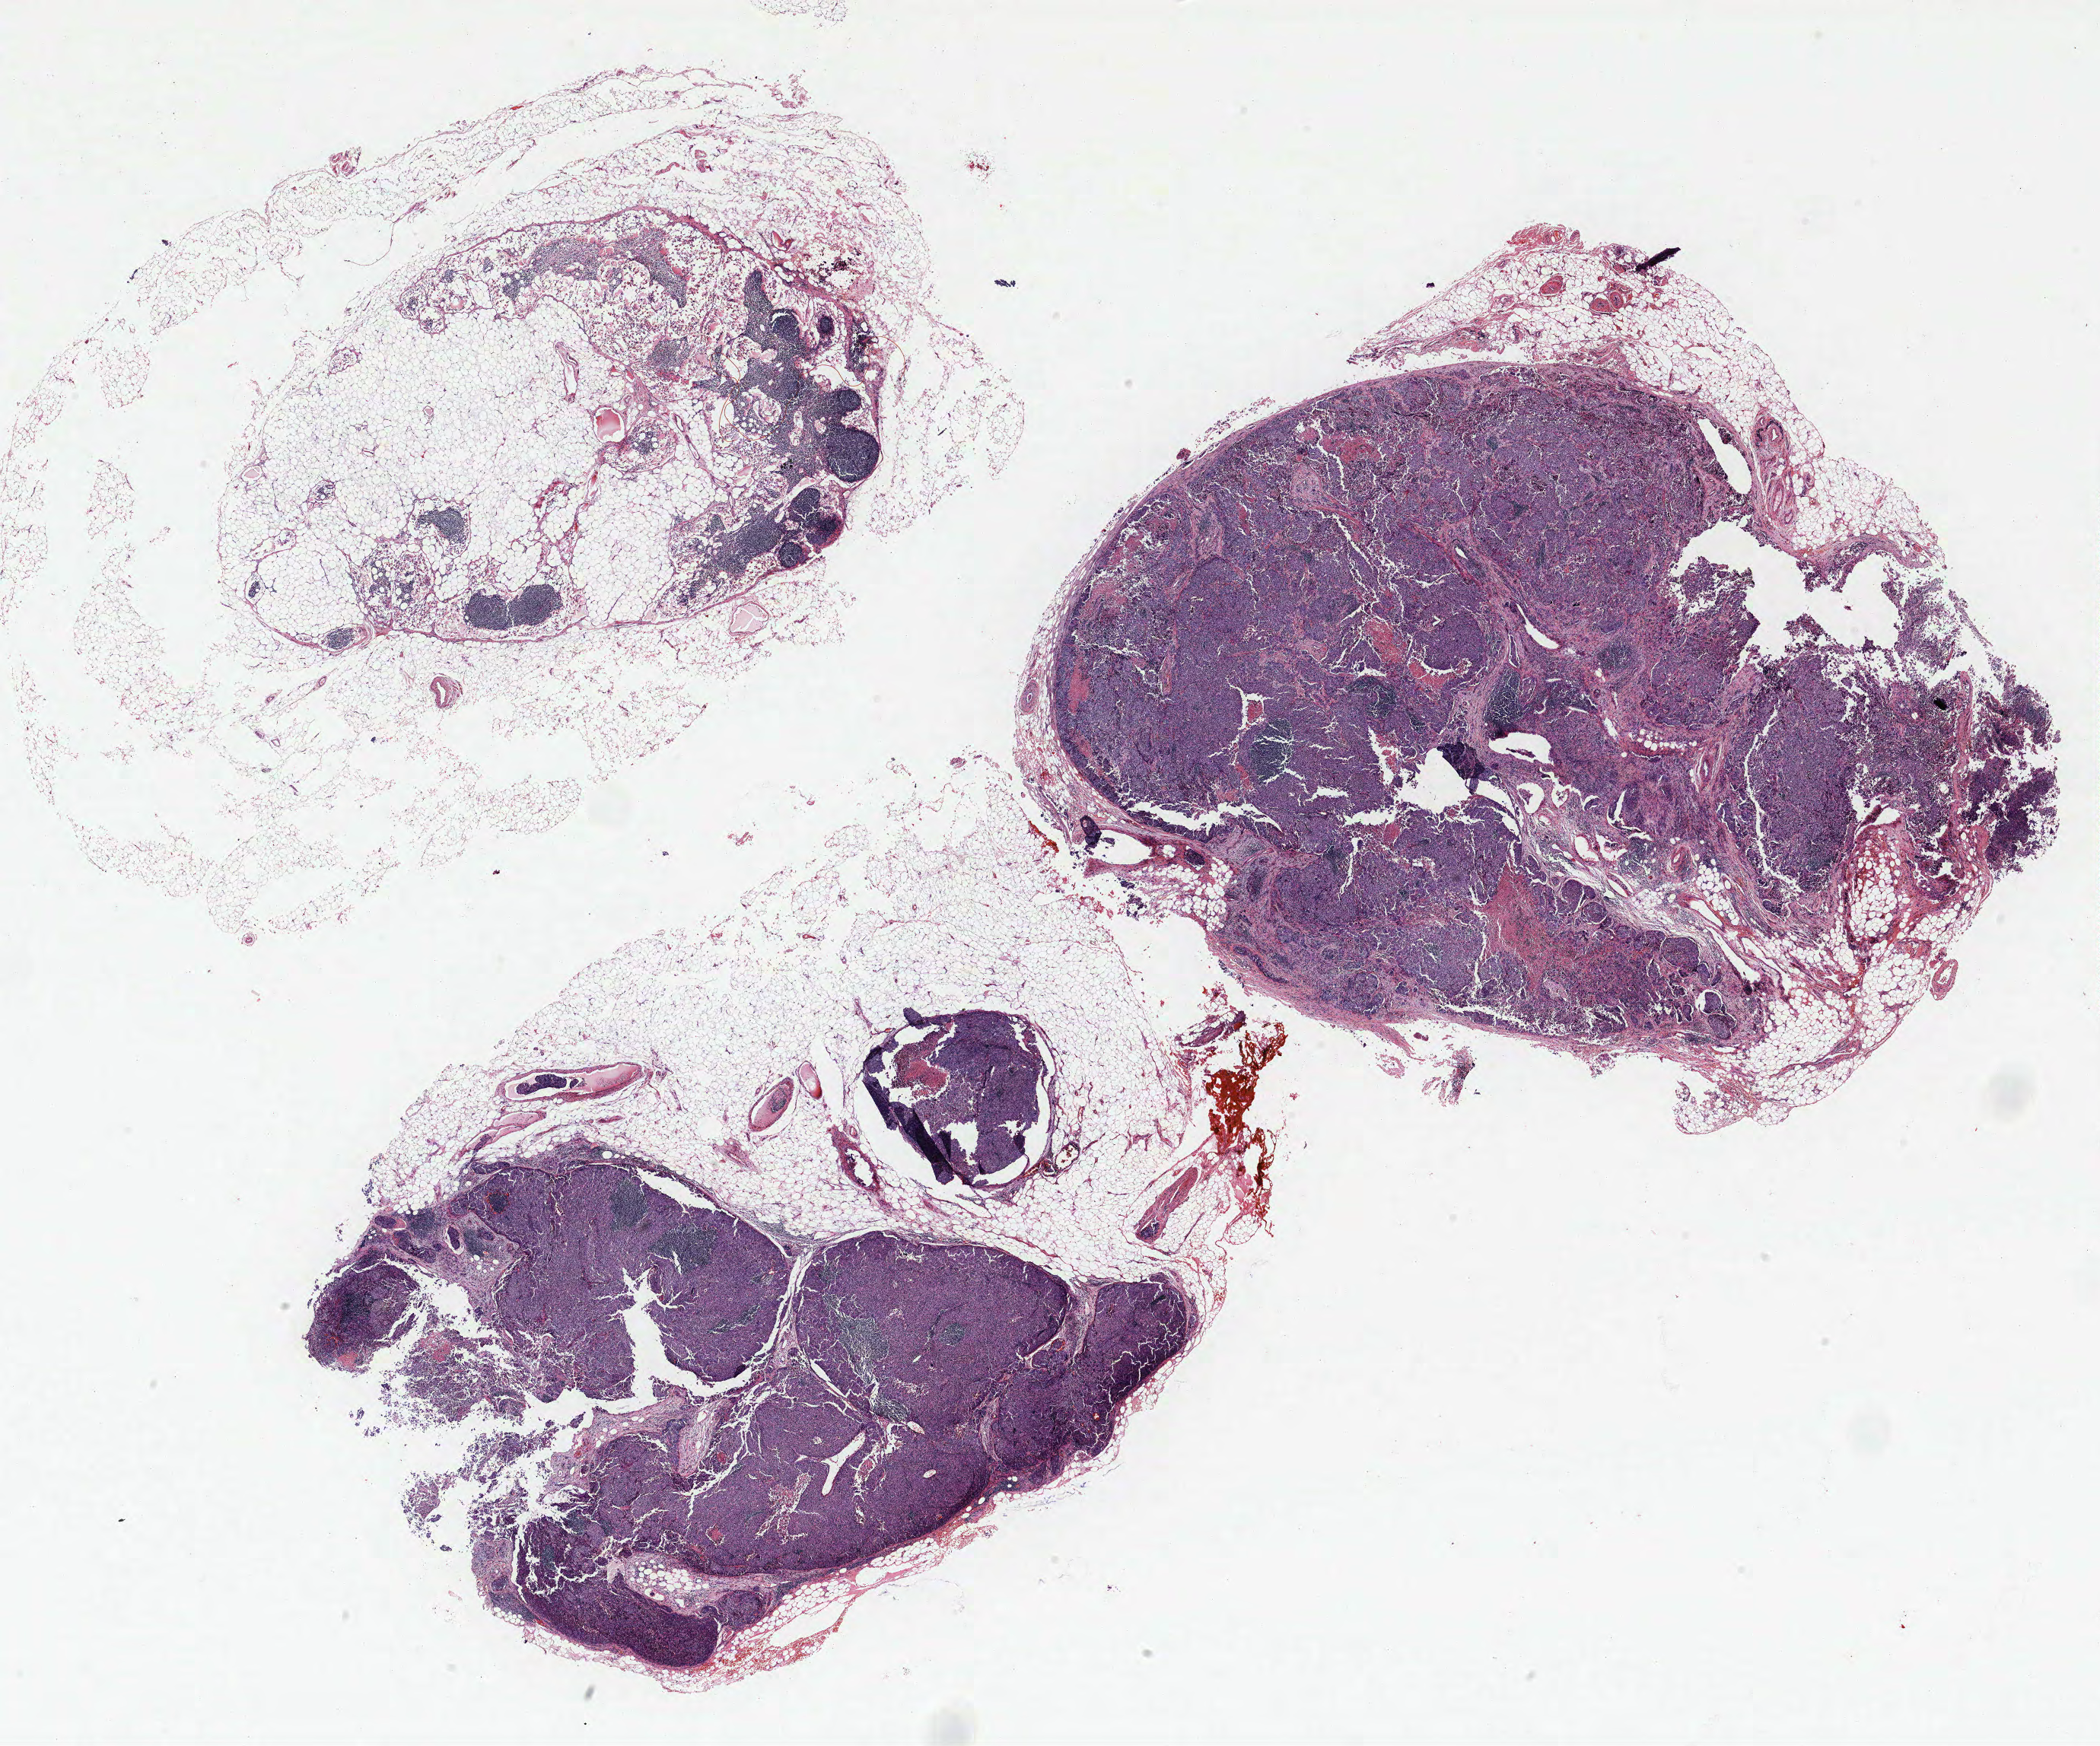
Whole-slide histology image, H&E, whole scanned area (about 22.1 x 18.4 mm, slide scanned at 40x) shown as a low-resolution overview, formalin-fixed paraffin-embedded (FFPE) section, lung. Male patient, aged 59 at enrolment.
Participant's lung-cancer diagnosis: Squamous cell carcinoma, NOS.